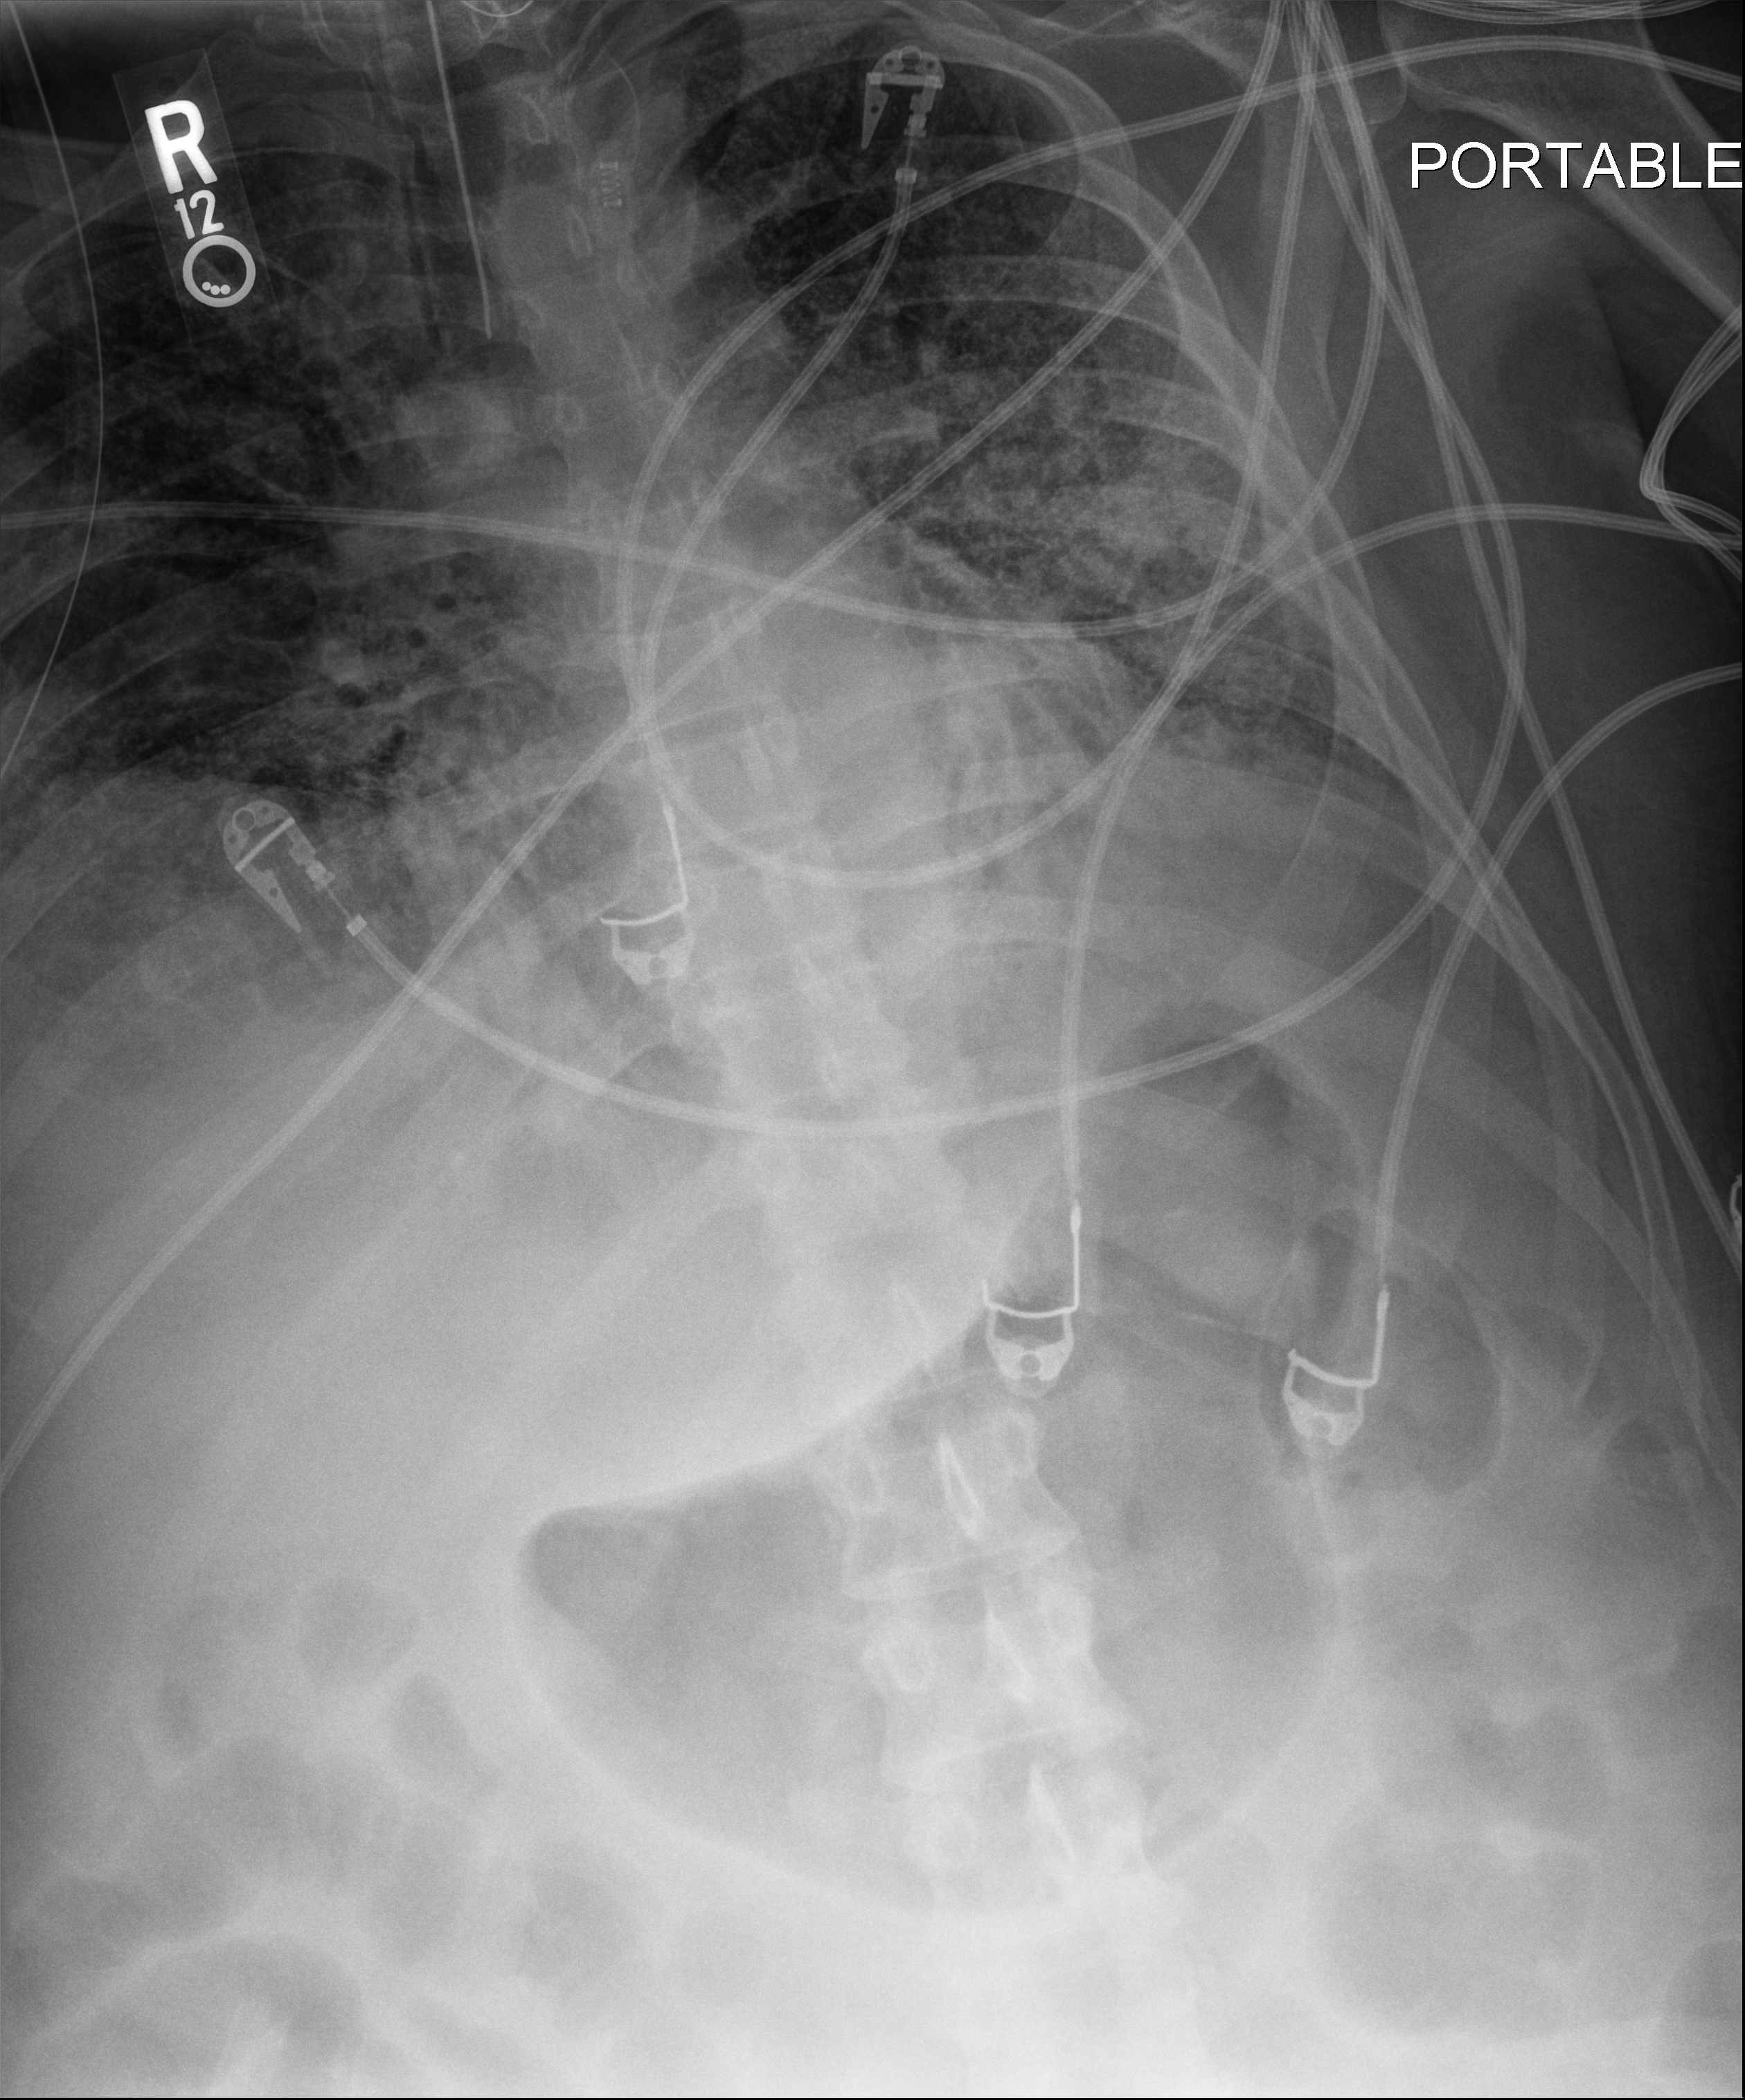
Bedside chest radiograph (digital radiography), anteroposterior (AP) projection. Male patient hospitalised with COVID-19, age 18–59 years.
Admission-level facts for this patient (not findings on this image; timing relative to this image not recorded):
- mechanically ventilated during this hospital stay: yes